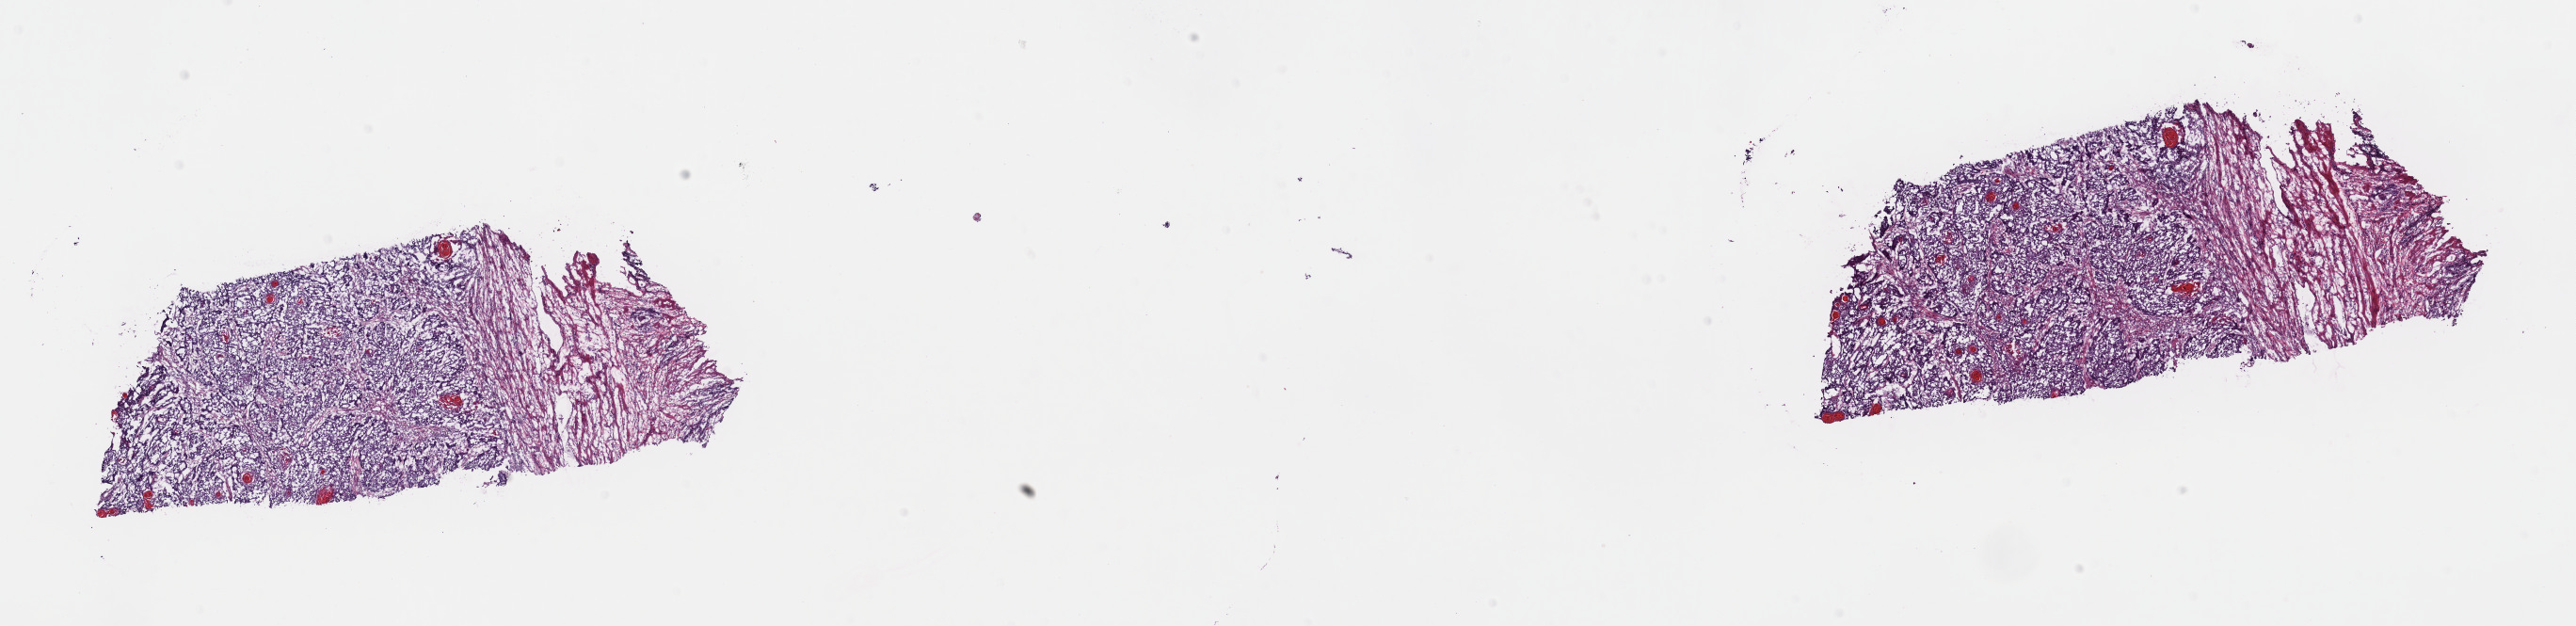
Hematoxylin and eosin (H&E) stained whole-slide image, shown as a low-resolution overview of the whole scanned area (about 21.6 x 5.3 mm); frozen section from the top of the tissue portion; sample: primary tumour, esophagus. Male, age 46 years at initial diagnosis. Composition of this section per pathologist review: tumour cells 80%, tumour nuclei 80%.
Histologic diagnosis: Squamous cell carcinoma, NOS (lower third of esophagus).